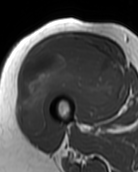
MRI of an extremity soft-tissue mass, one axial slice. Position 45 of 99 along the scan axis. MR volume resampled by the dataset authors to the PET/CT grid (not the native acquisition matrix). 3.27 mm slice thickness. 138 × 172 image matrix, field of view 135 × 168 mm. Female patient. From the clinical record (not read from this slice): histological type: pleiomorphic undifferentiated sarcoma; grade: high; site of the primary tumour: right quadricep.
Outlined on this slice (expert contour drawn on MRI and transferred to this co-registered scan by the dataset authors):
- gross tumour volume including surrounding oedema: bounding box <21,34,122,135> (left, top, right, bottom; pixels)
- gross tumour volume (mass): <21,34,122,135>